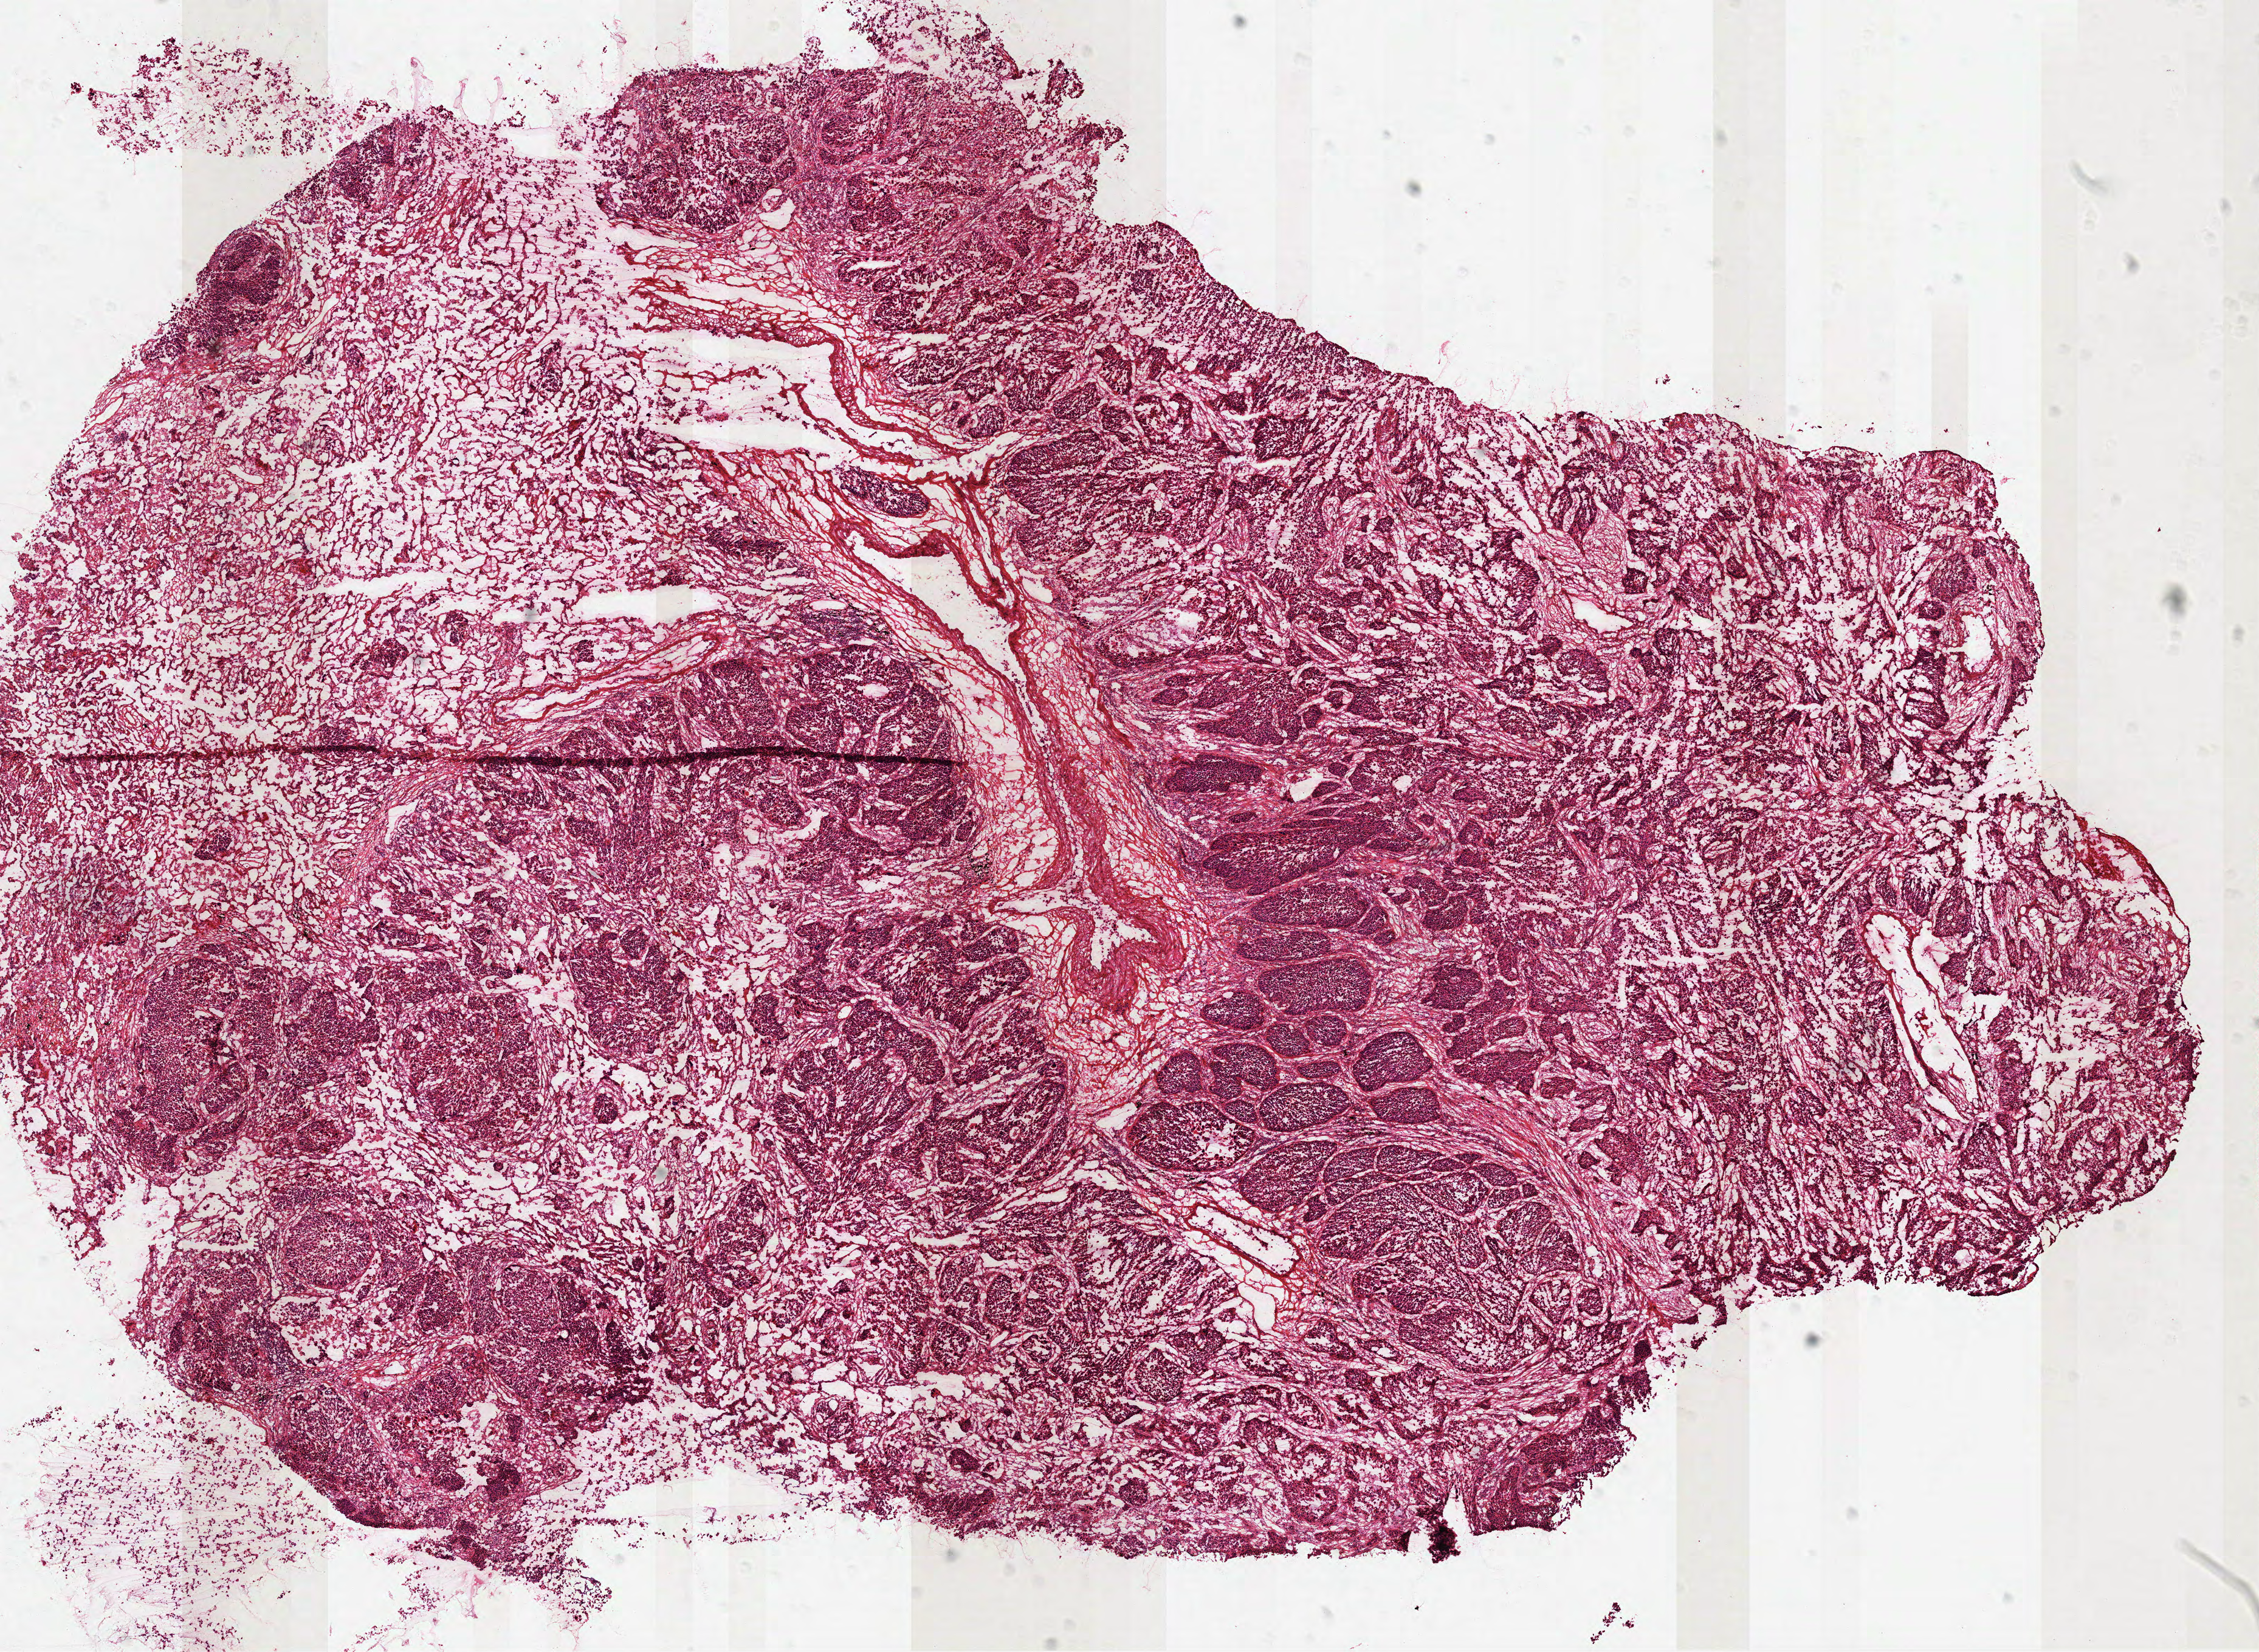
Digitized H&E-stained tissue section (whole slide), low-resolution overview of the scanned area, about 15.0 x 11.0 mm; frozen section from the top of the tissue portion; lung, primary tumour sample. Male, age 67 years at initial diagnosis. Composition of this section per pathologist review: tumour cells 75%, tumour nuclei 70%, normal cells 15%, stromal cells 10%, necrosis 0%.
AJCC pathologic stage: IV (7th edition). Histologic diagnosis: Squamous cell carcinoma, NOS. Laterality: left.